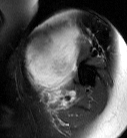
MRI of an extremity soft-tissue mass, one axial slice. Slice 53 of 87 in the series (ordered by position). T2-weighted fat-saturated. MR volume resampled by the dataset authors to the PET/CT grid (not the native acquisition matrix). 127 × 138 image matrix, field of view 124 × 135 mm. Female patient. From the clinical record (not read from this slice): histological type: pleiomorphic leiomyosarcoma; grade: high; site of the primary tumour: left biceps.
Outlined on this slice (expert contour drawn on MRI and transferred to this co-registered scan by the dataset authors):
- gross tumour volume including surrounding oedema: bounding box <24,27,83,108> (left, top, right, bottom; pixels)
- gross tumour volume (mass): <24,27,80,92>